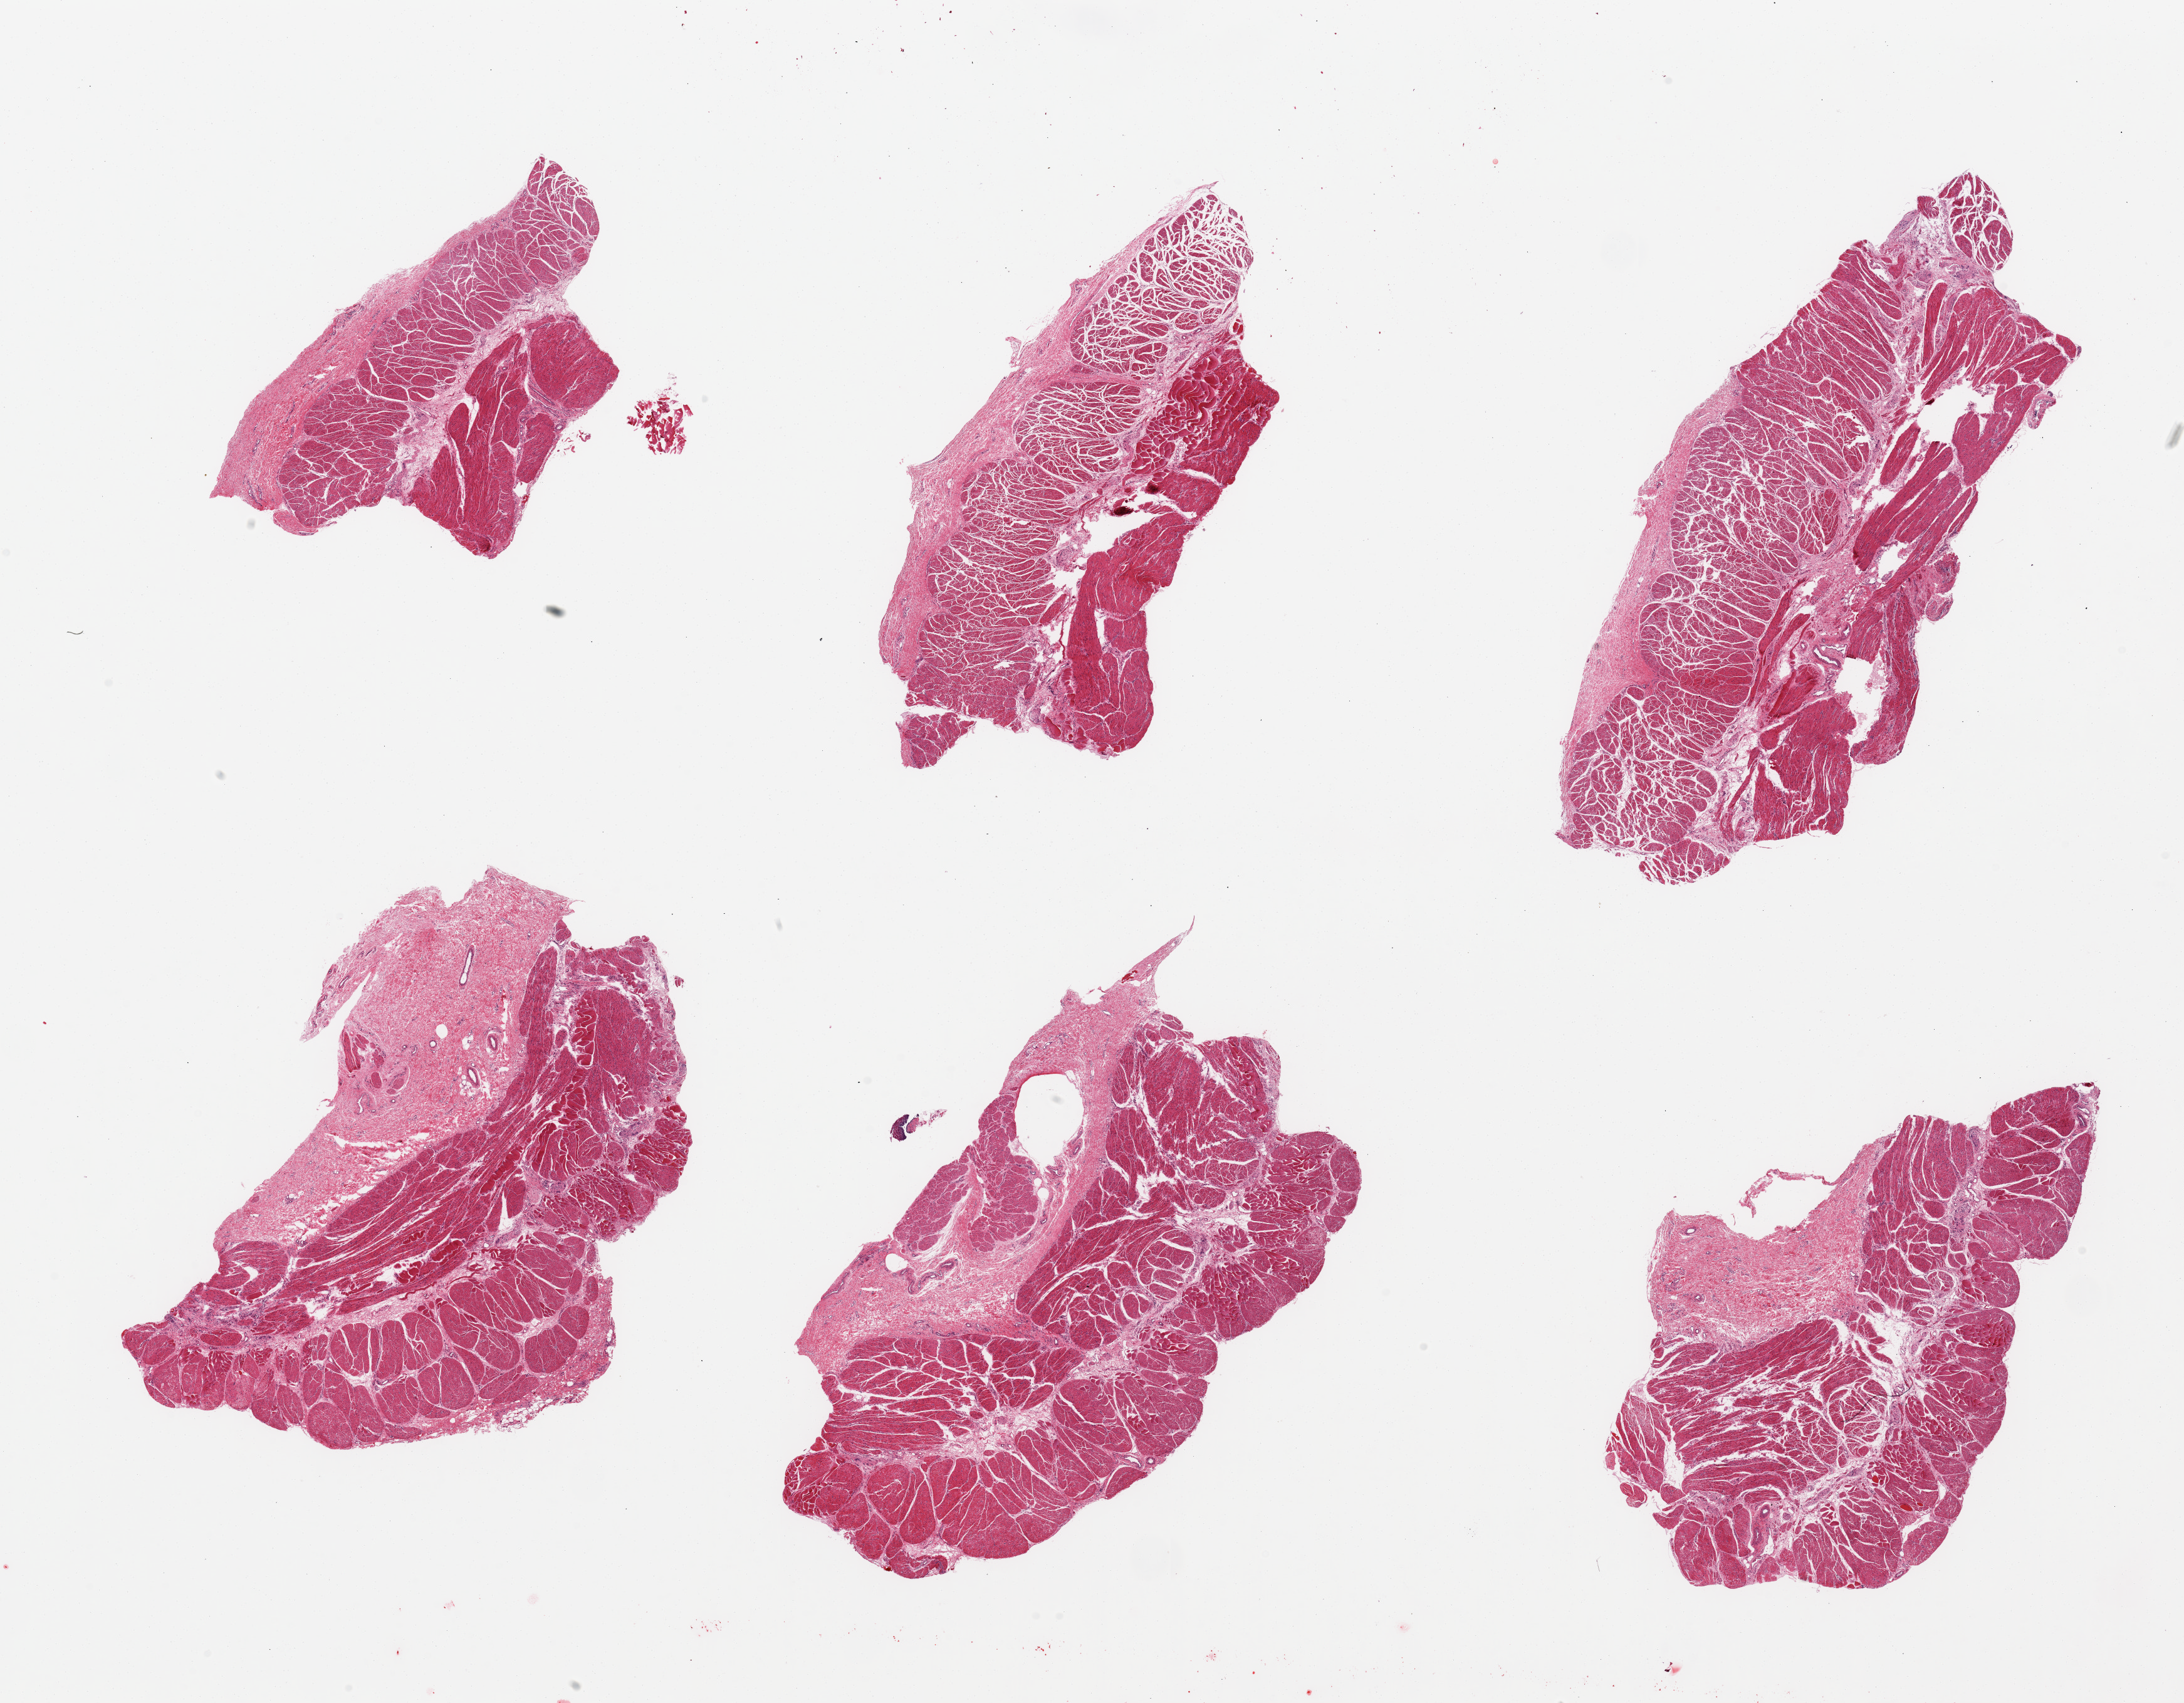
Hematoxylin and eosin (H&E) whole-slide image, brightfield — whole scanned area (about 27.6 x 21.5 mm) shown as a low-resolution overview; PAXgene-fixed paraffin-embedded (PFPE) section; target tissue: esophageal muscle; donor tissue sample. Donor sex: male.
Reviewer comment on this tissue sample: 6 pieces; includes major admixture of smooth and skeletal muscle indicating sampling of upper esophagus.